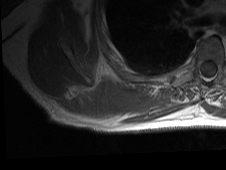
MRI of an extremity soft-tissue mass, one axial slice; position 20 of 81 along the scan axis; MR volume resampled by the dataset authors to the PET/CT grid (not the native acquisition matrix); 3.27 mm slice thickness; 226 × 170 image matrix, field of view 221 × 166 mm. Male patient. From the clinical record (not read from this slice): histological type: pleiomorphic spindle cell undifferentiated; grade: high; site of the primary tumour: right parascapusular.
Annotated regions visible in this slice (expert contour drawn on MRI and transferred to this co-registered scan by the dataset authors):
- gross tumour volume including surrounding oedema: box from (x=58, y=79) to (x=186, y=123) px
- gross tumour volume (mass): (x=85, y=81)–(x=125, y=114)